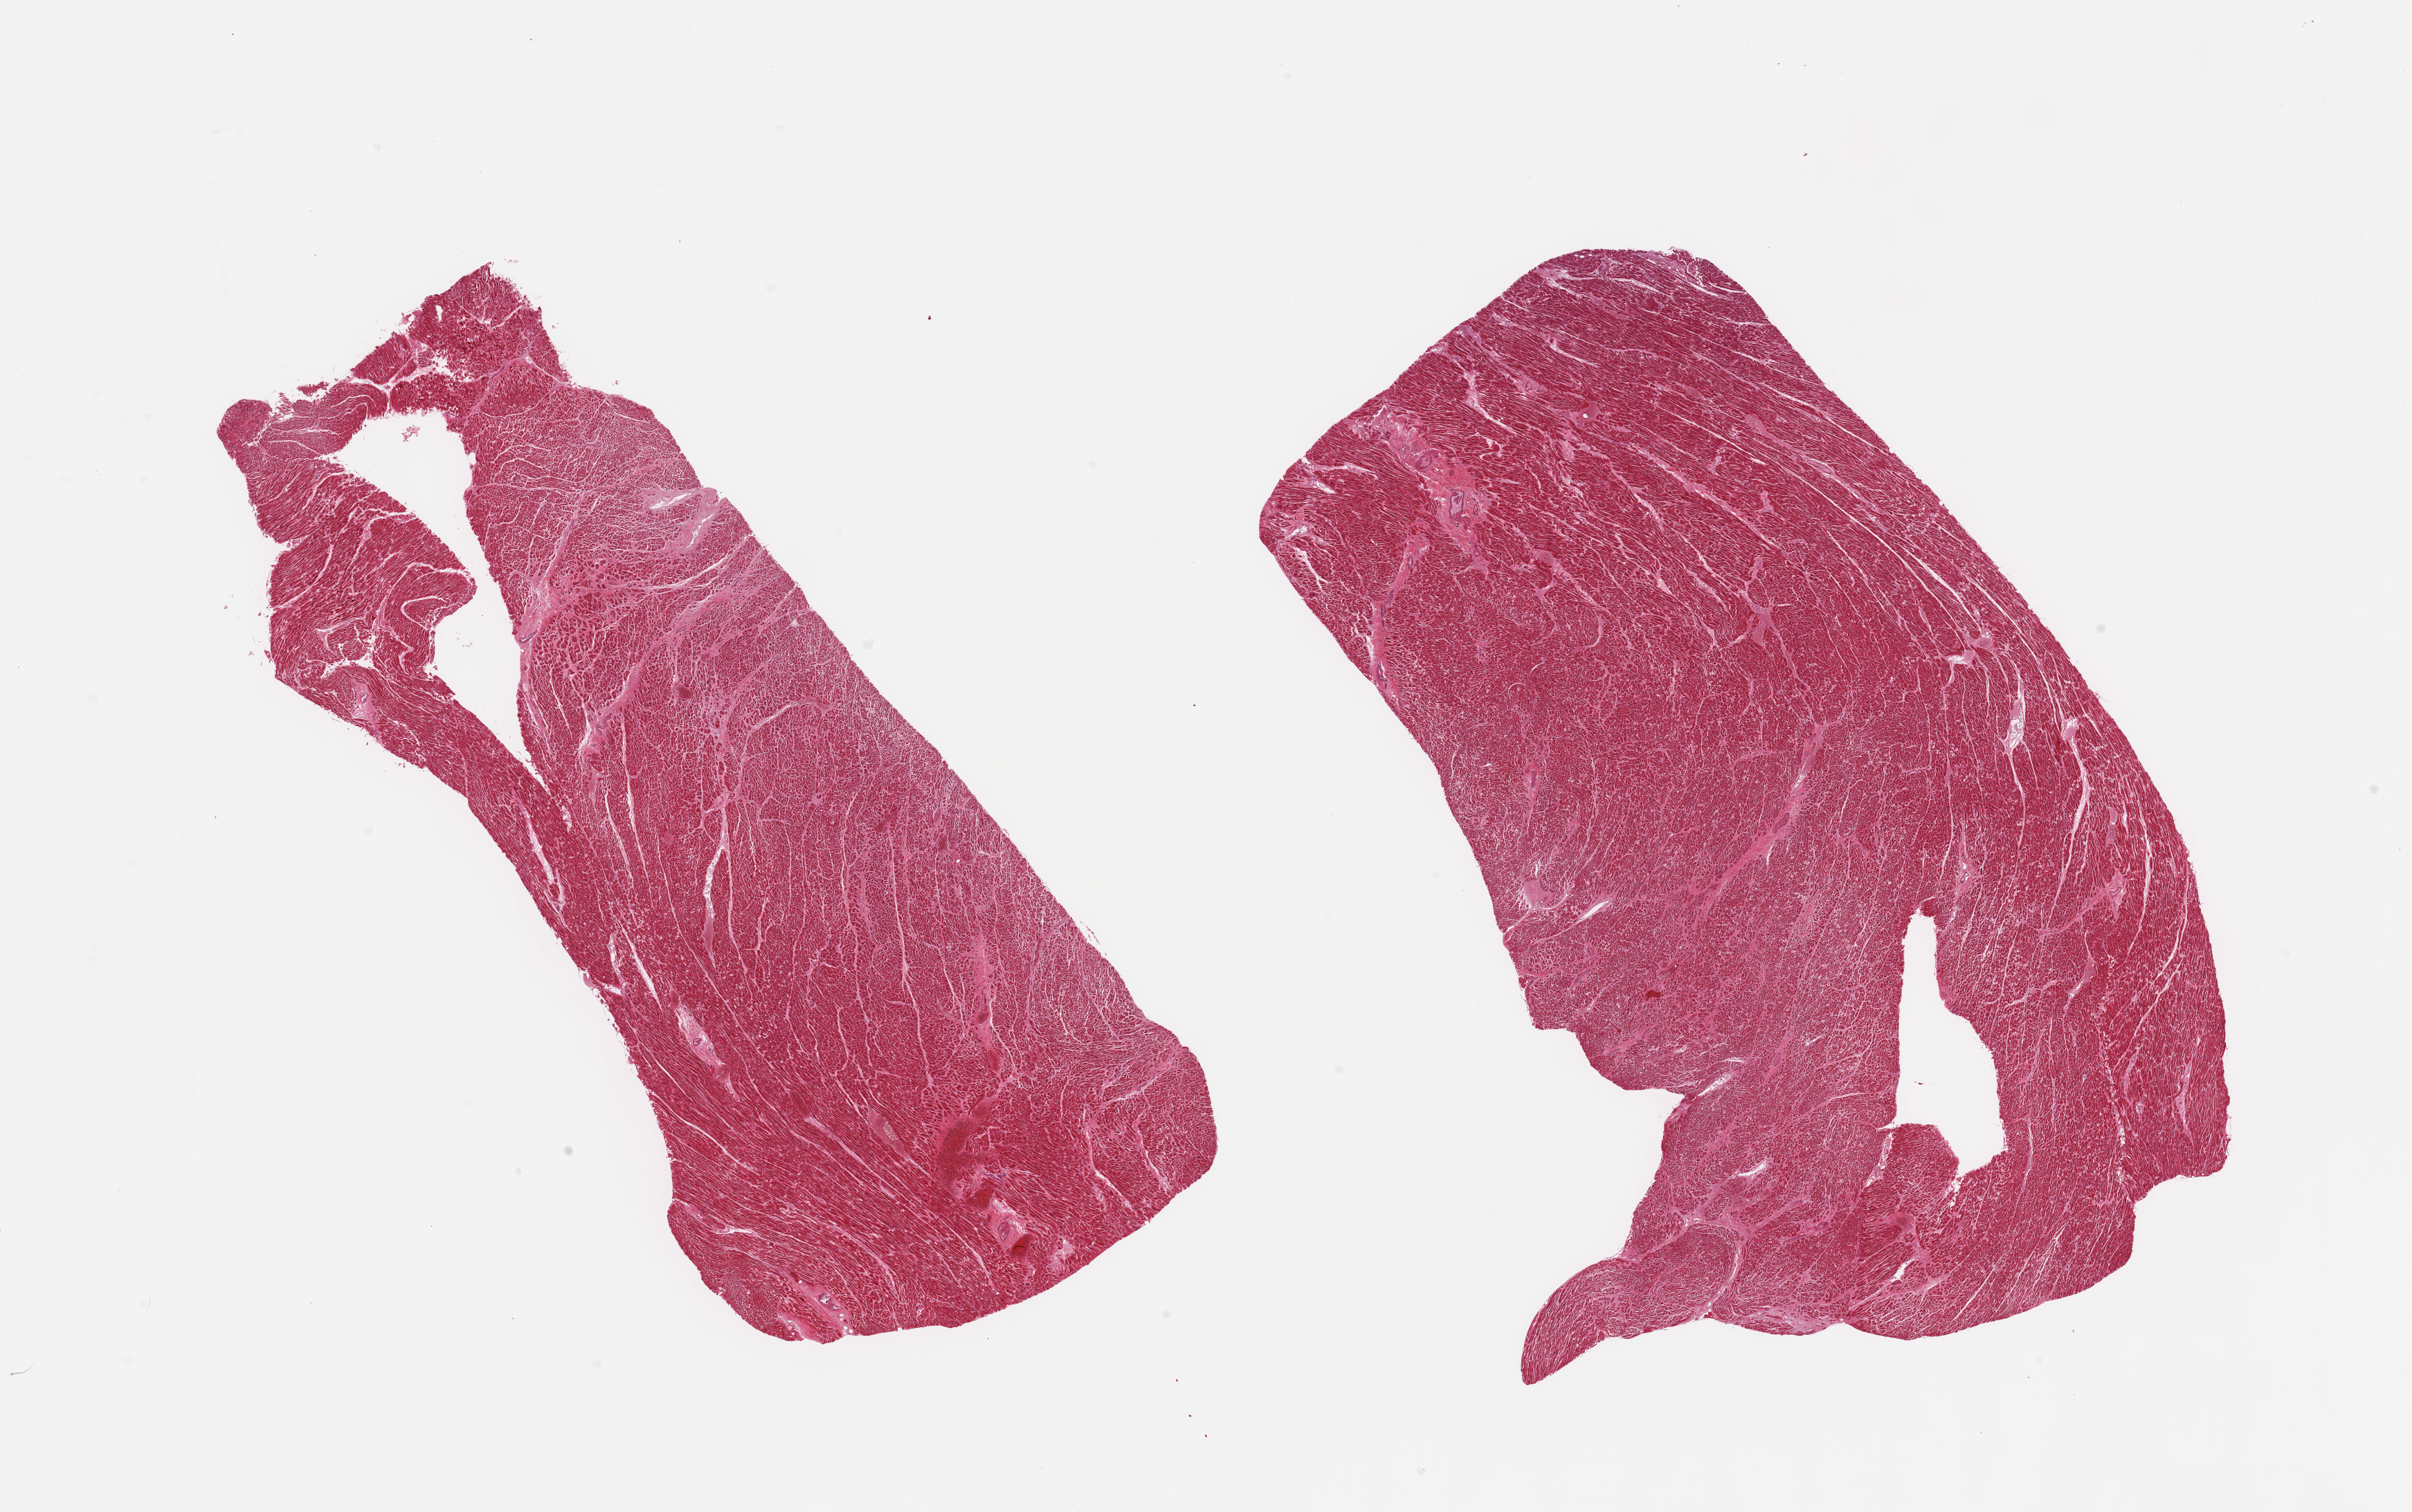
Whole-slide image, H&E stain, brightfield, shown as a low-resolution overview of the whole scanned area (about 27.6 x 17.3 mm, from a 20x scan). PAXgene-fixed paraffin-embedded (PFPE) section. Section of heart (target tissue). Donor tissue sample.
• review note (as recorded): 2 pieces, moderate chronic ischemic changes/interstitial fibrosis, focal microinfarcts